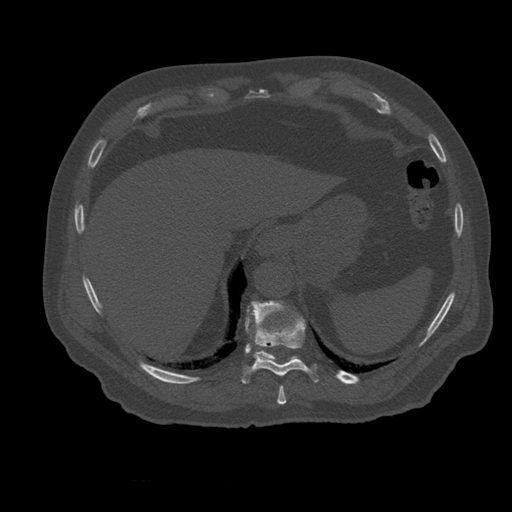
CT including the spine, one axial slice; position 299 of 399 along the scan axis; reconstruction kernel STANDARD; 120 kVp; bone window (W 1800 / L 400 HU); 1.25 mm slice thickness; 512 × 512 image matrix, field of view 407 × 407 mm. Patient age 73 years. Case-level facts recorded for this patient, not image findings: primary cancer: prostate.
Annotated regions visible in this slice (semi-automatic segmentation, software-assisted and operator-edited):
- T10 vertebra: bounding box <241,317,319,384> (left, top, right, bottom; pixels)
- T11 vertebra: <246,301,295,362>
- T9 vertebra: <277,386,287,405>